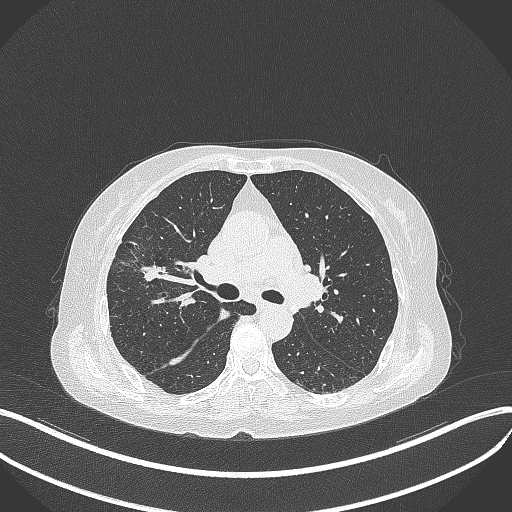
Chest CT, one axial slice. Reconstruction kernel B70f. 120 kVp. Lung window (W 1500 / L -600 HU). 1 mm slice thickness. 512 × 512 image matrix. Patient: female, 69 years. From the clinical record (not read from this slice): clinical TNM (as recorded): T1b N3 M0.
Outlined on this slice (rectangle marked by the reading radiologist):
- lung tumour (recorded histology: small cell carcinoma): box from (x=131, y=257) to (x=173, y=287) px